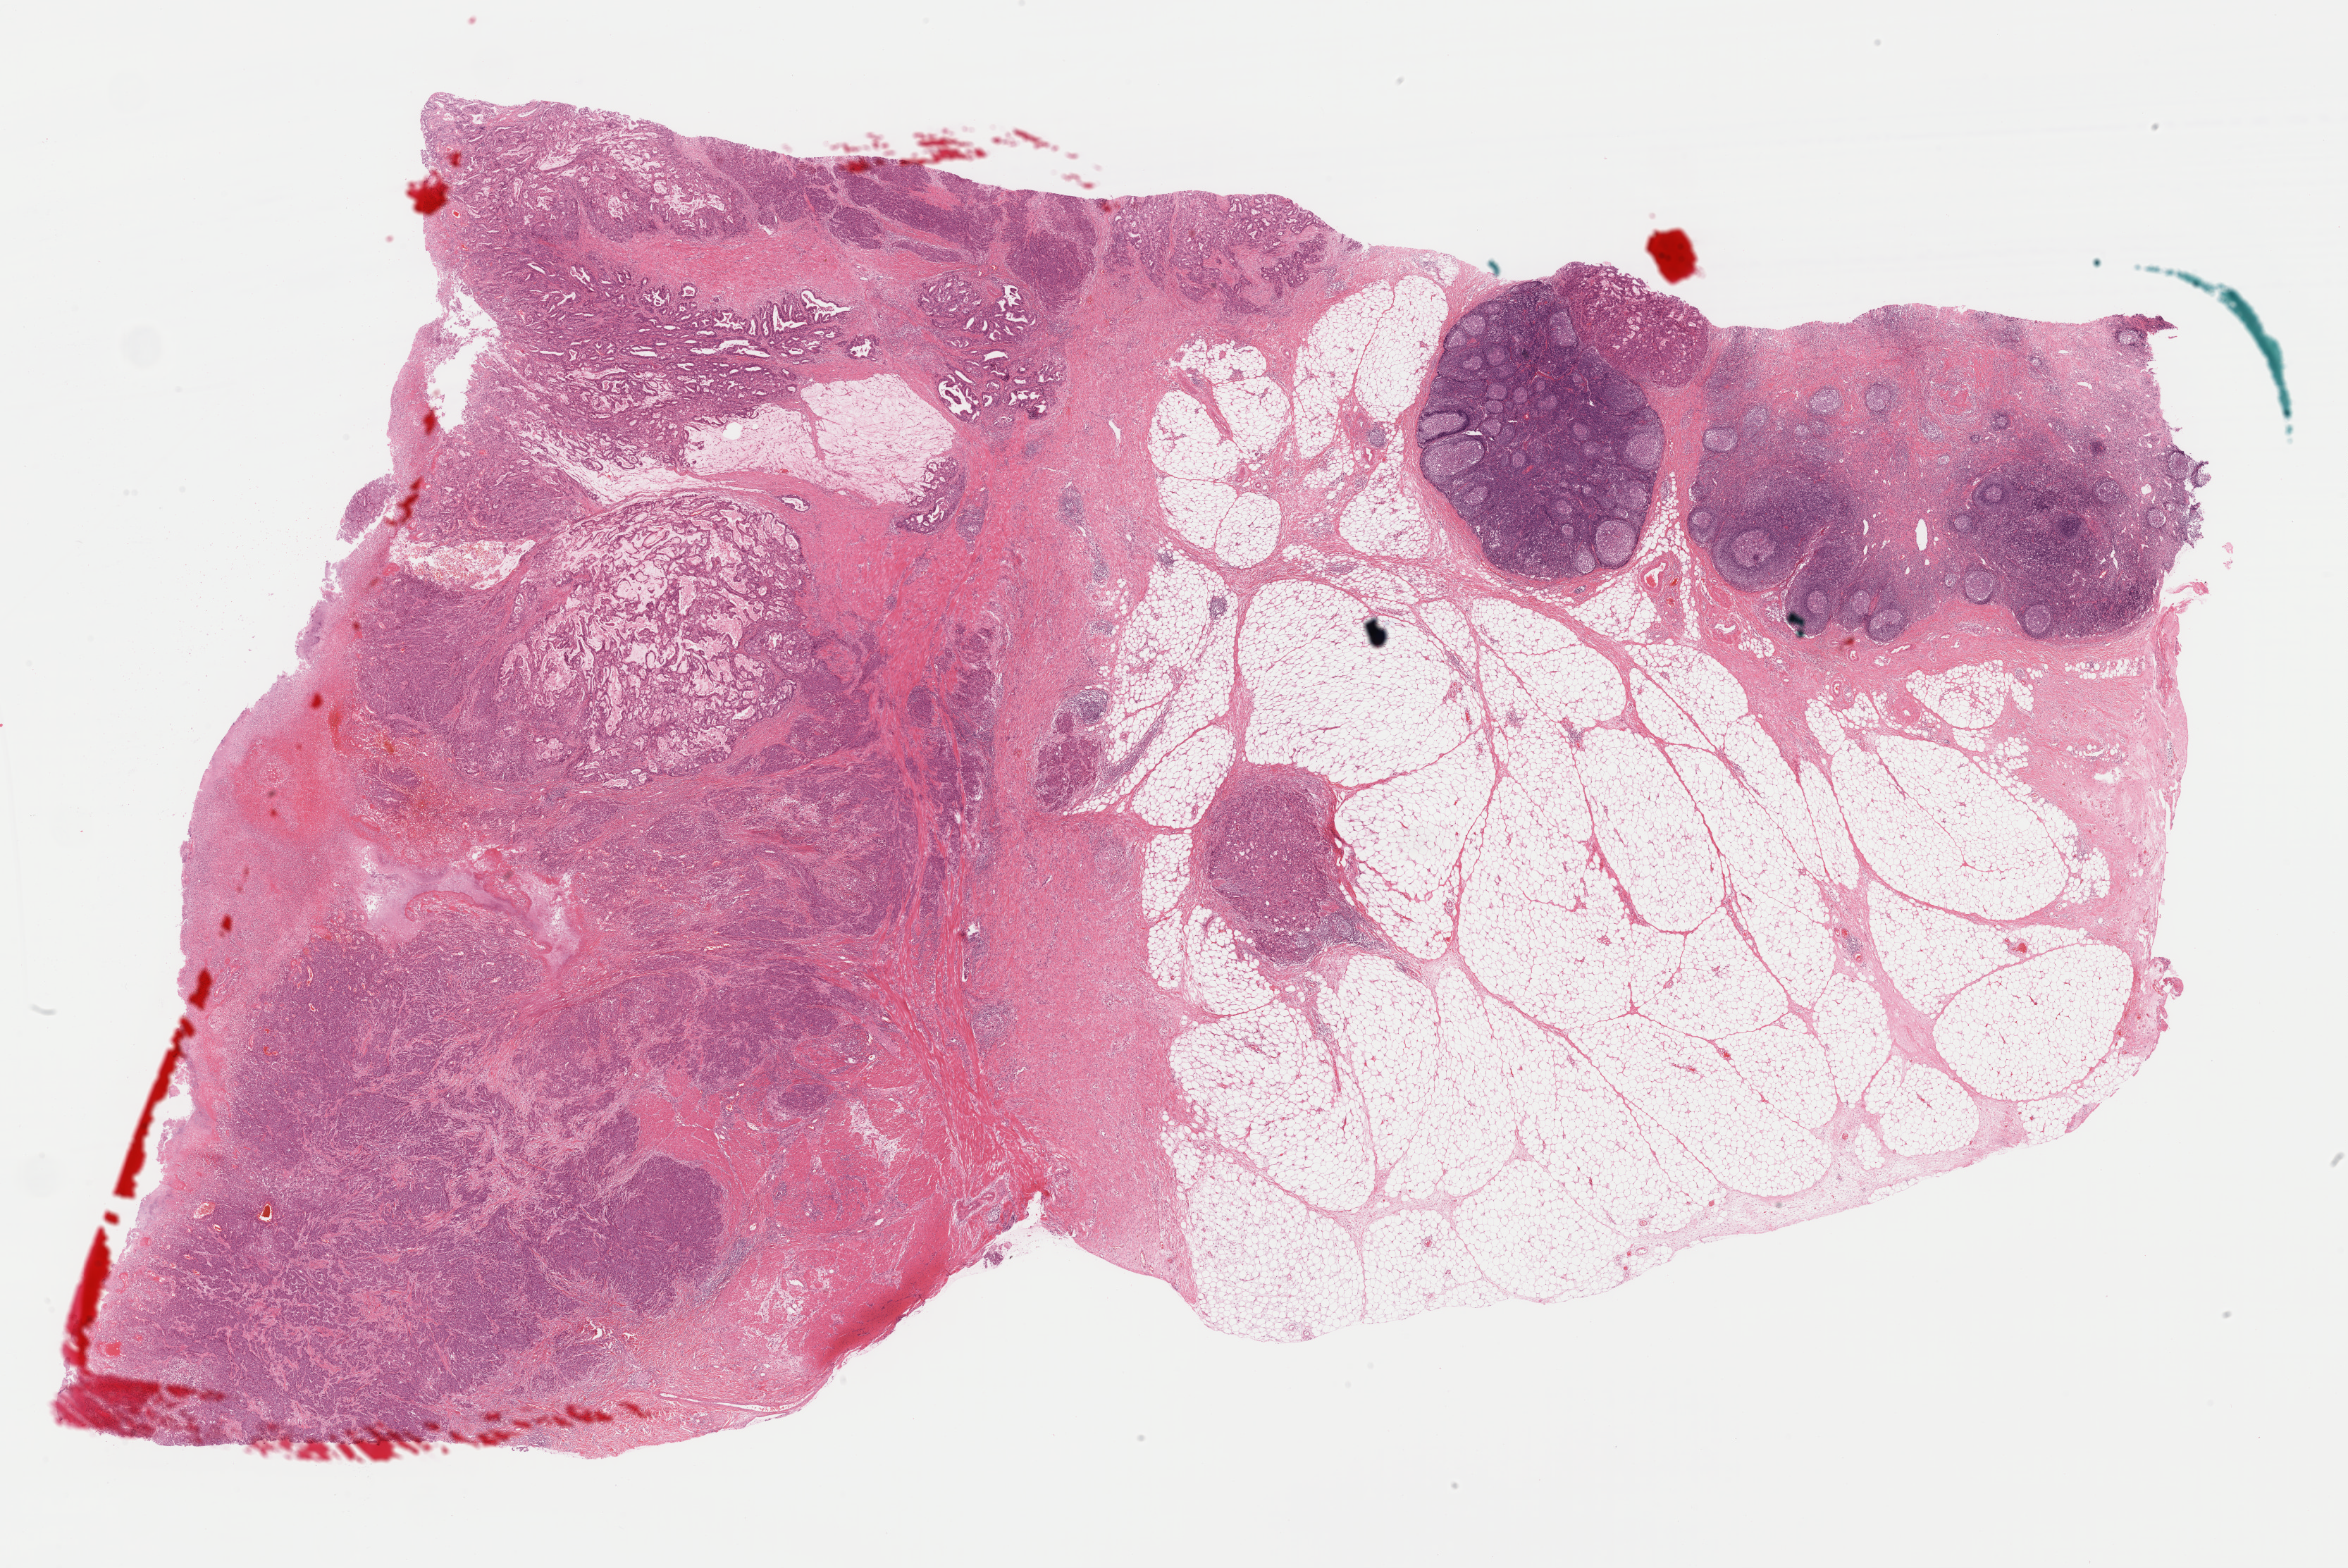
Whole-slide histology image, H&E-stained, whole scanned area (about 26.3 x 17.6 mm, from a 40x scan) shown as a low-resolution overview; formalin-fixed paraffin-embedded (FFPE) diagnostic section; primary tumour sample from the stomach. Female, age 75 years at initial diagnosis. Histologic grade: G2 (moderately differentiated).
* AJCC pathologic stage: IIIB (7th edition)
* histologic diagnosis: Adenocarcinoma, NOS (gastric antrum)